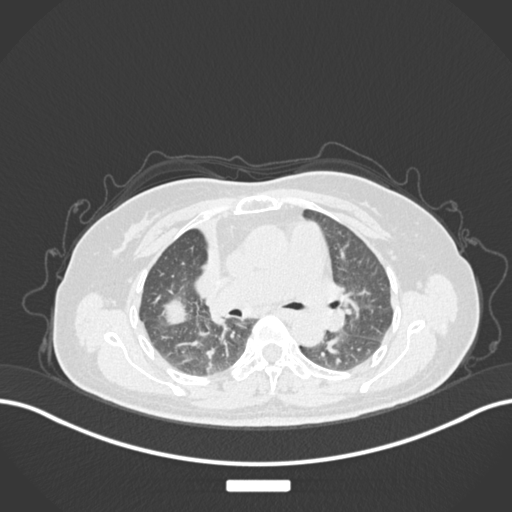
Chest CT, one axial slice. Position 90 of 177 along the scan axis. Reconstruction kernel B30f. Lung window (W 1500 / L -600 HU). 1 mm slice thickness. 512 × 512 image matrix, field of view 400 × 400 mm. Female patient, age 60 years. From the clinical record (not read from this slice): clinical TNM (as recorded): T3 N1 M1.
Annotated regions visible in this slice (bounding box drawn by a radiologist):
- lung tumour (recorded histology: adenocarcinoma): bounding box [x1, y1, x2, y2] px = [149, 289, 201, 331]